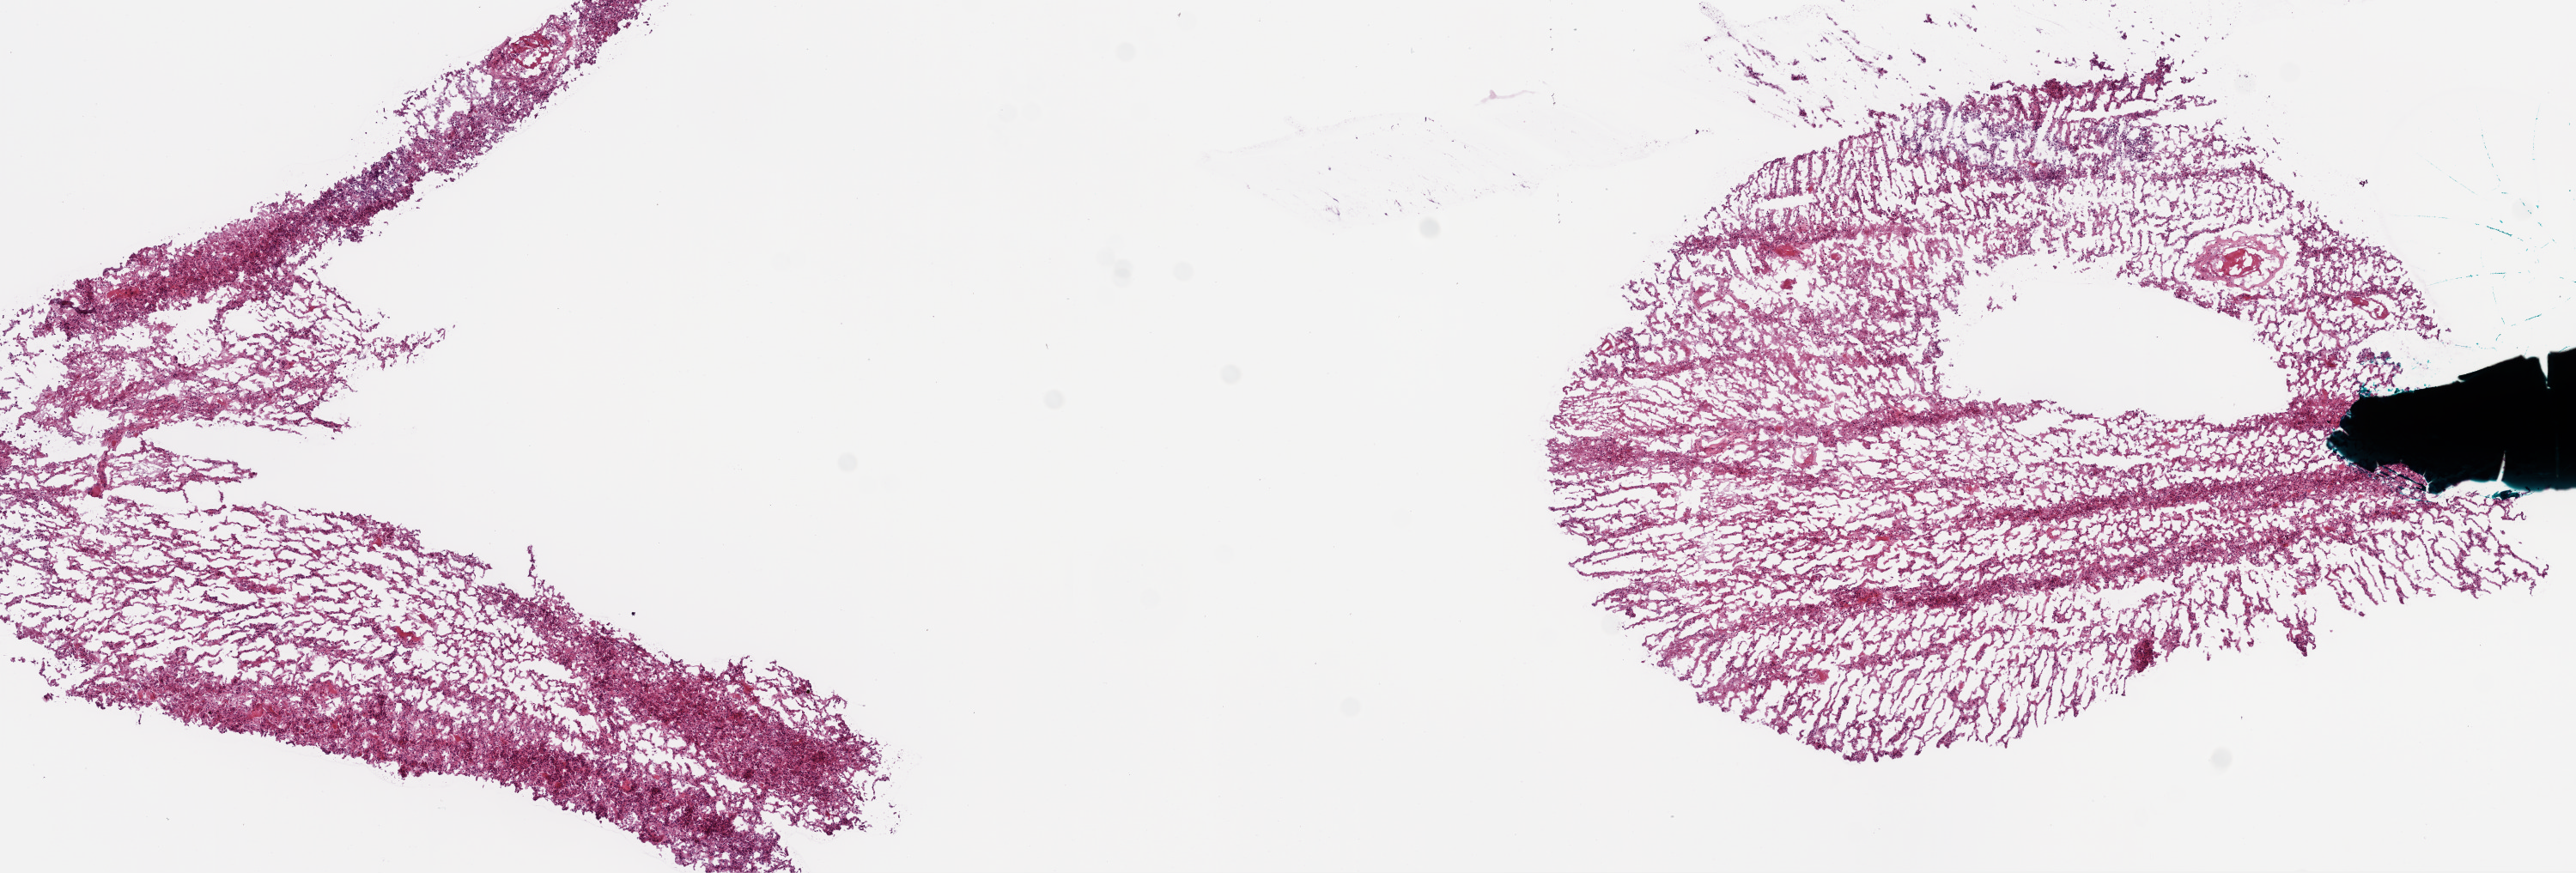
H&E-stained whole-slide image, low-resolution overview of the scanned area, about 12.0 x 4.1 mm (slide scanned at 20x), frozen section from the bottom of the tissue portion, sample: primary tumour, brain. Patient: female, age at initial diagnosis 60 years. Pathologist review of this section (percent, as recorded): tumour cells 60%, tumour nuclei 85%, normal cells 0%, stromal cells 10%, necrosis 30%.
Histologic diagnosis: Glioblastoma.